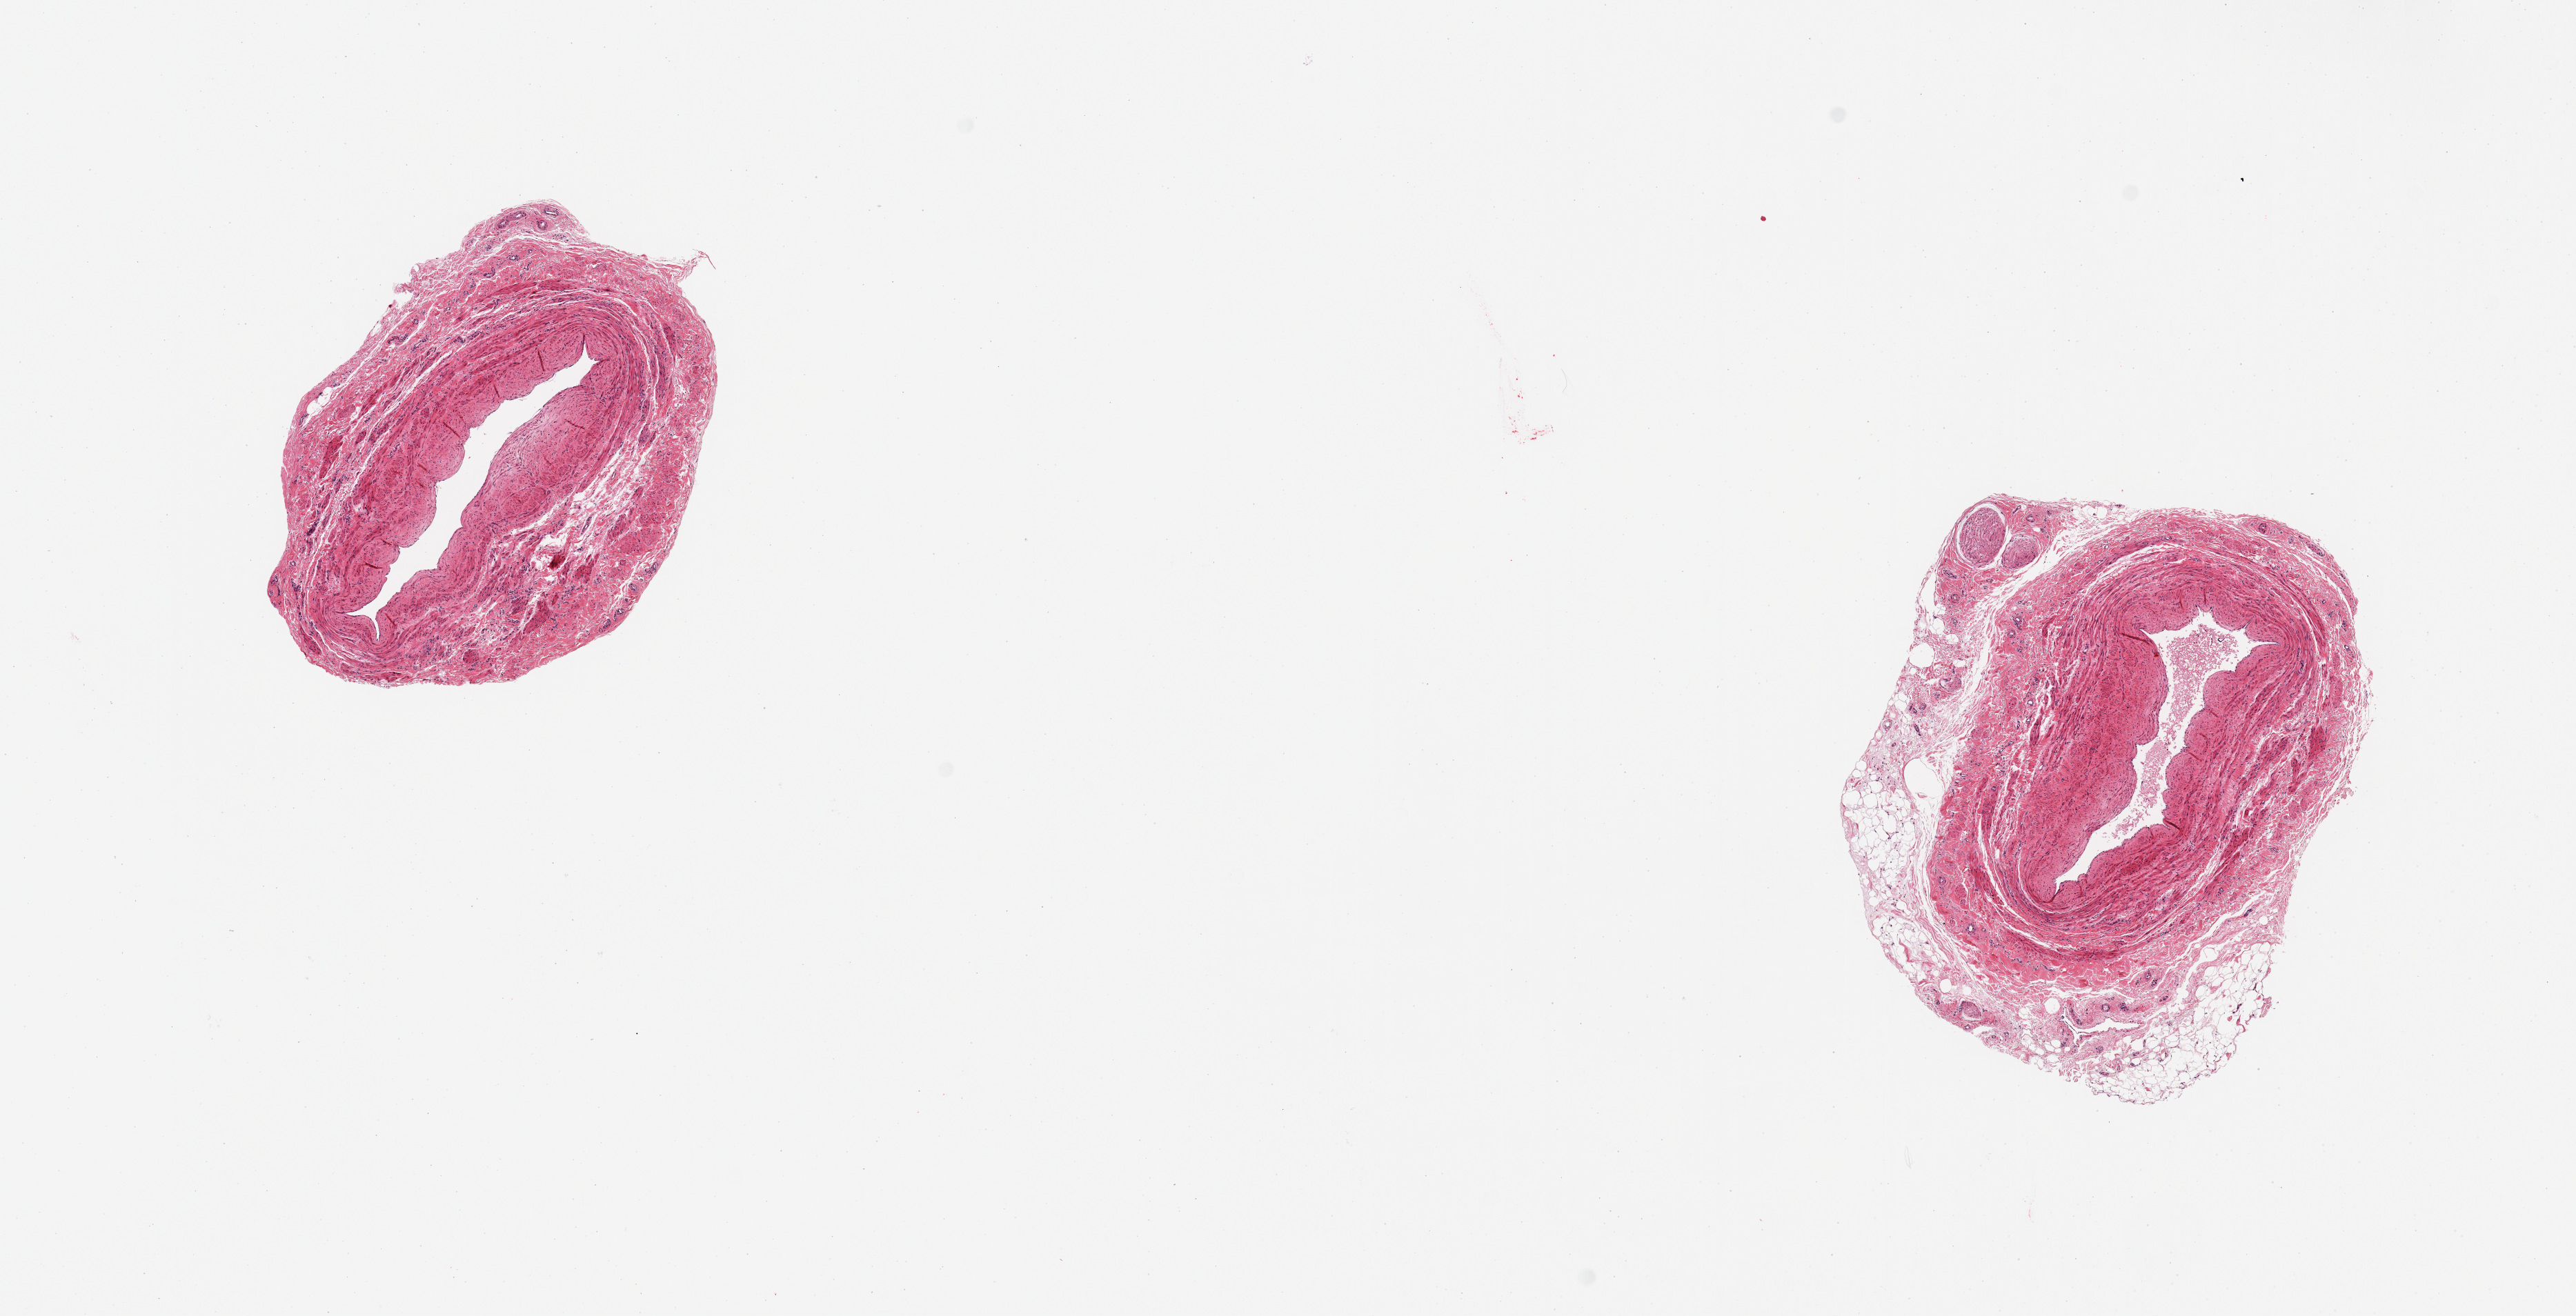
Whole-slide image, H&E stain — shown as a low-resolution overview of the whole scanned area (about 14.8 x 7.5 mm), PAXgene-fixed paraffin-embedded (PFPE) section, sampled site (target tissue): tibial artery, tissue donor sample. Donor sex: female.
* reviewer comment on this tissue sample: 2 pieces, rim of adherent fat/fibrous tissue/peripheral nerve up to ~0.8mm